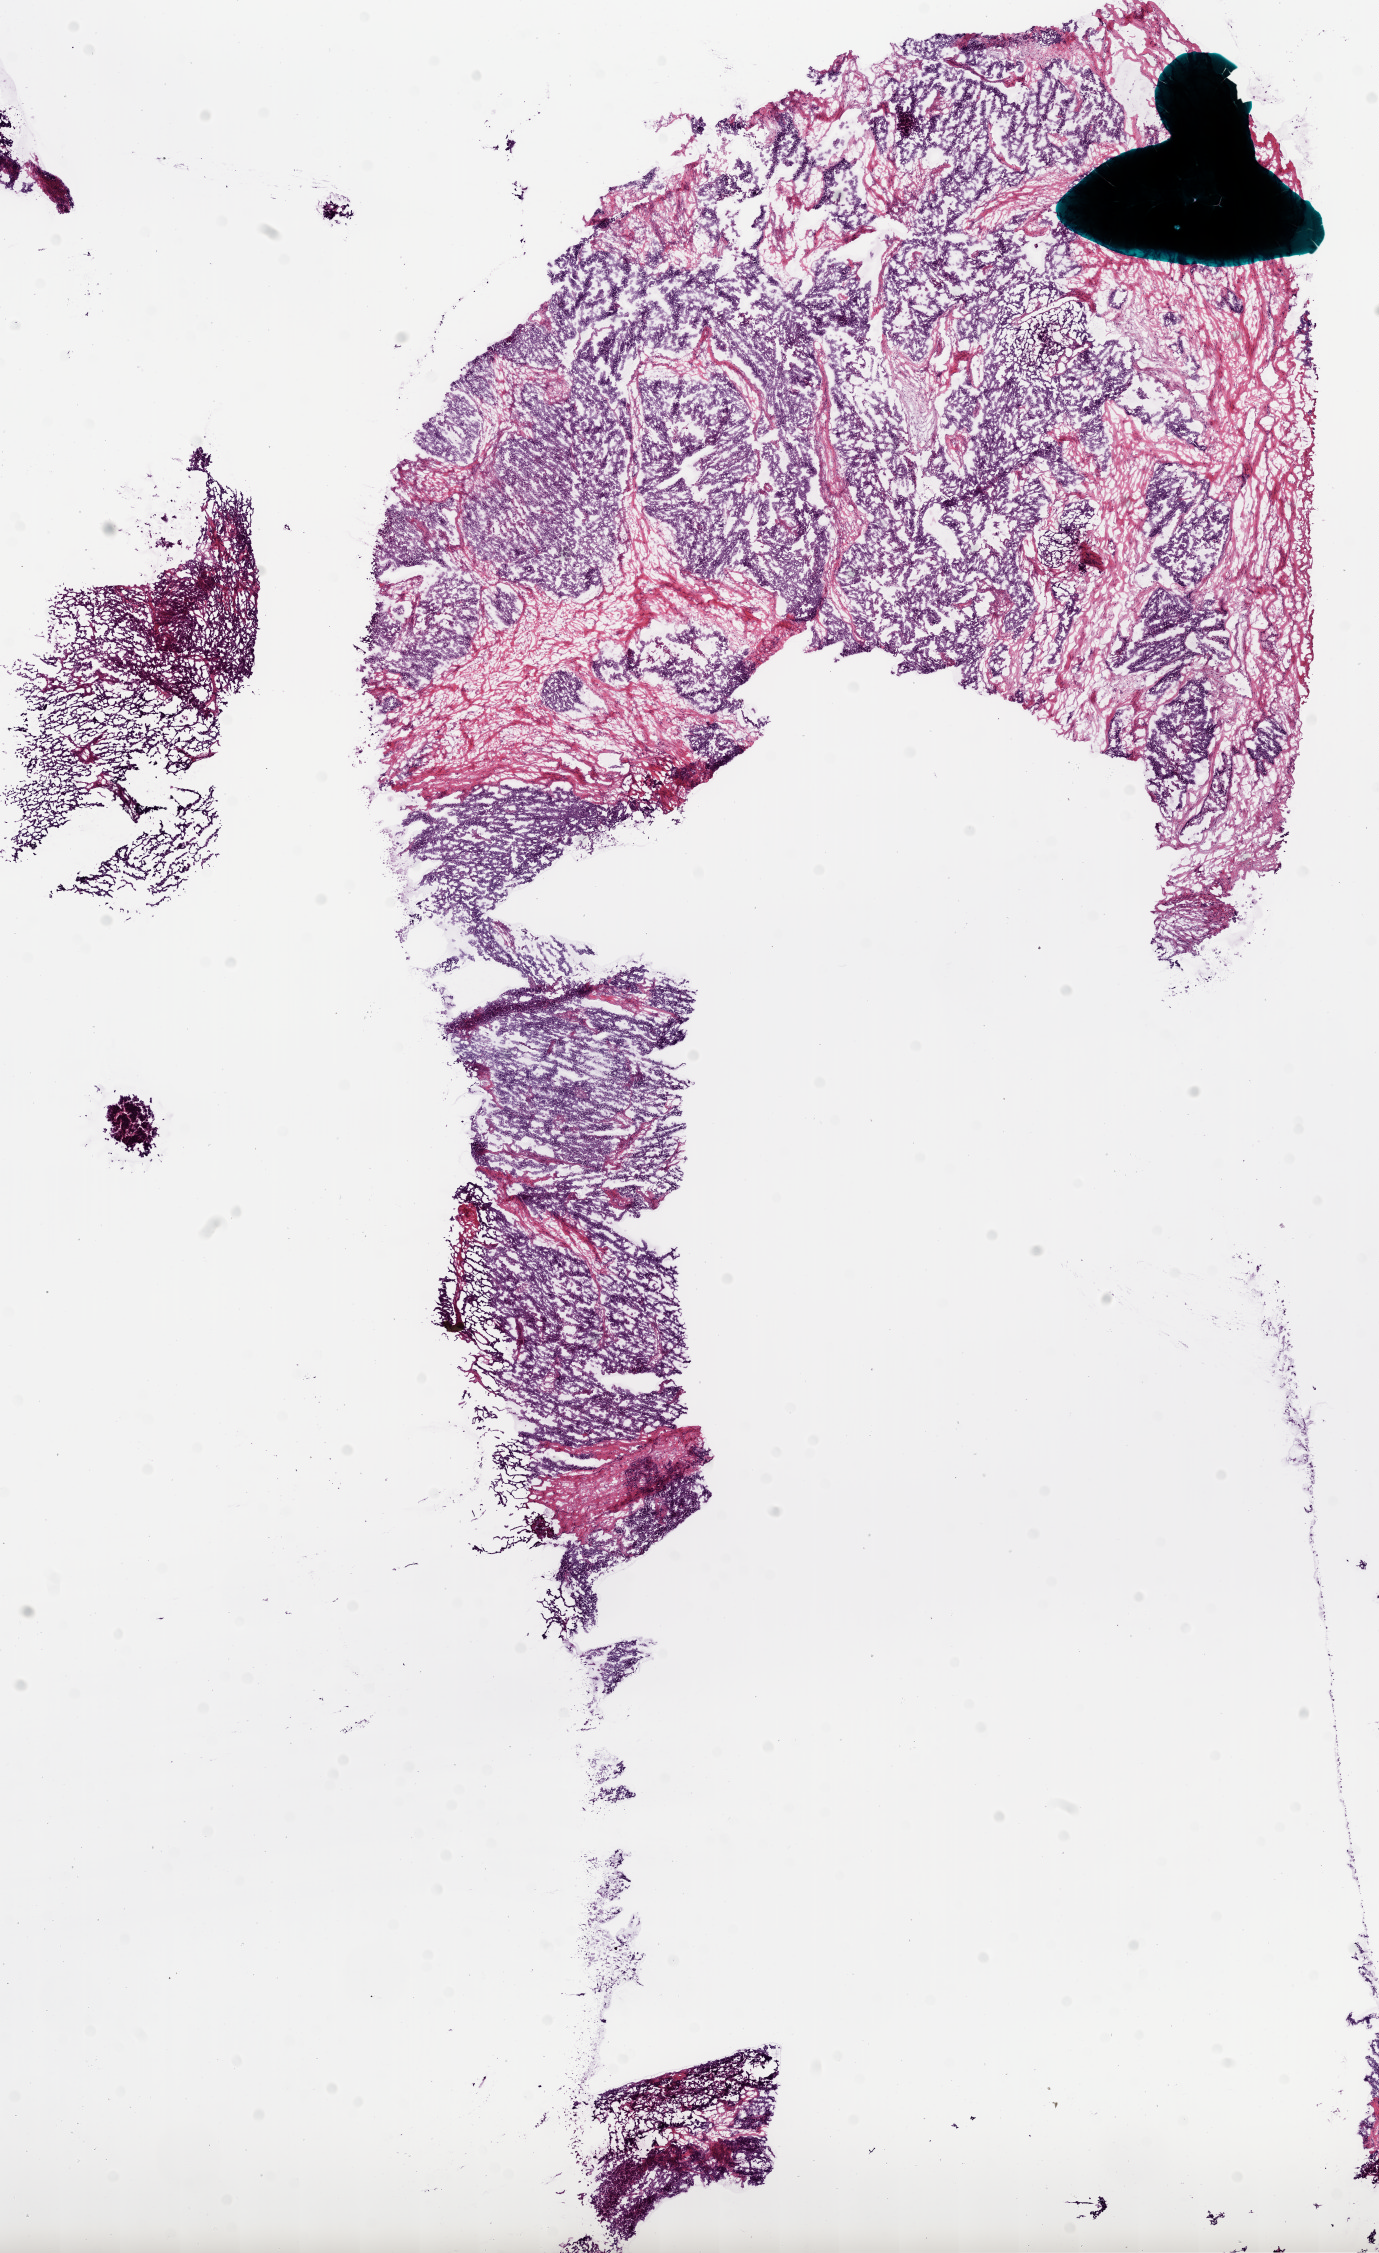
Digitized H&E-stained tissue section (whole slide), a low-resolution overview of the entire scanned area, about 11.1 x 18.2 mm (from a 20x scan), frozen section from the bottom of the tissue portion, ovary, primary tumour sample. Female patient; age at initial diagnosis 58 years. Histologic grade: G3 (poorly differentiated). Composition of this section per pathologist review: tumour cells 74%, tumour nuclei 75%, normal cells 0%, stromal cells 25%, necrosis 1%.
* FIGO stage: IIIC
* pathologic diagnosis: Serous cystadenocarcinoma, NOS